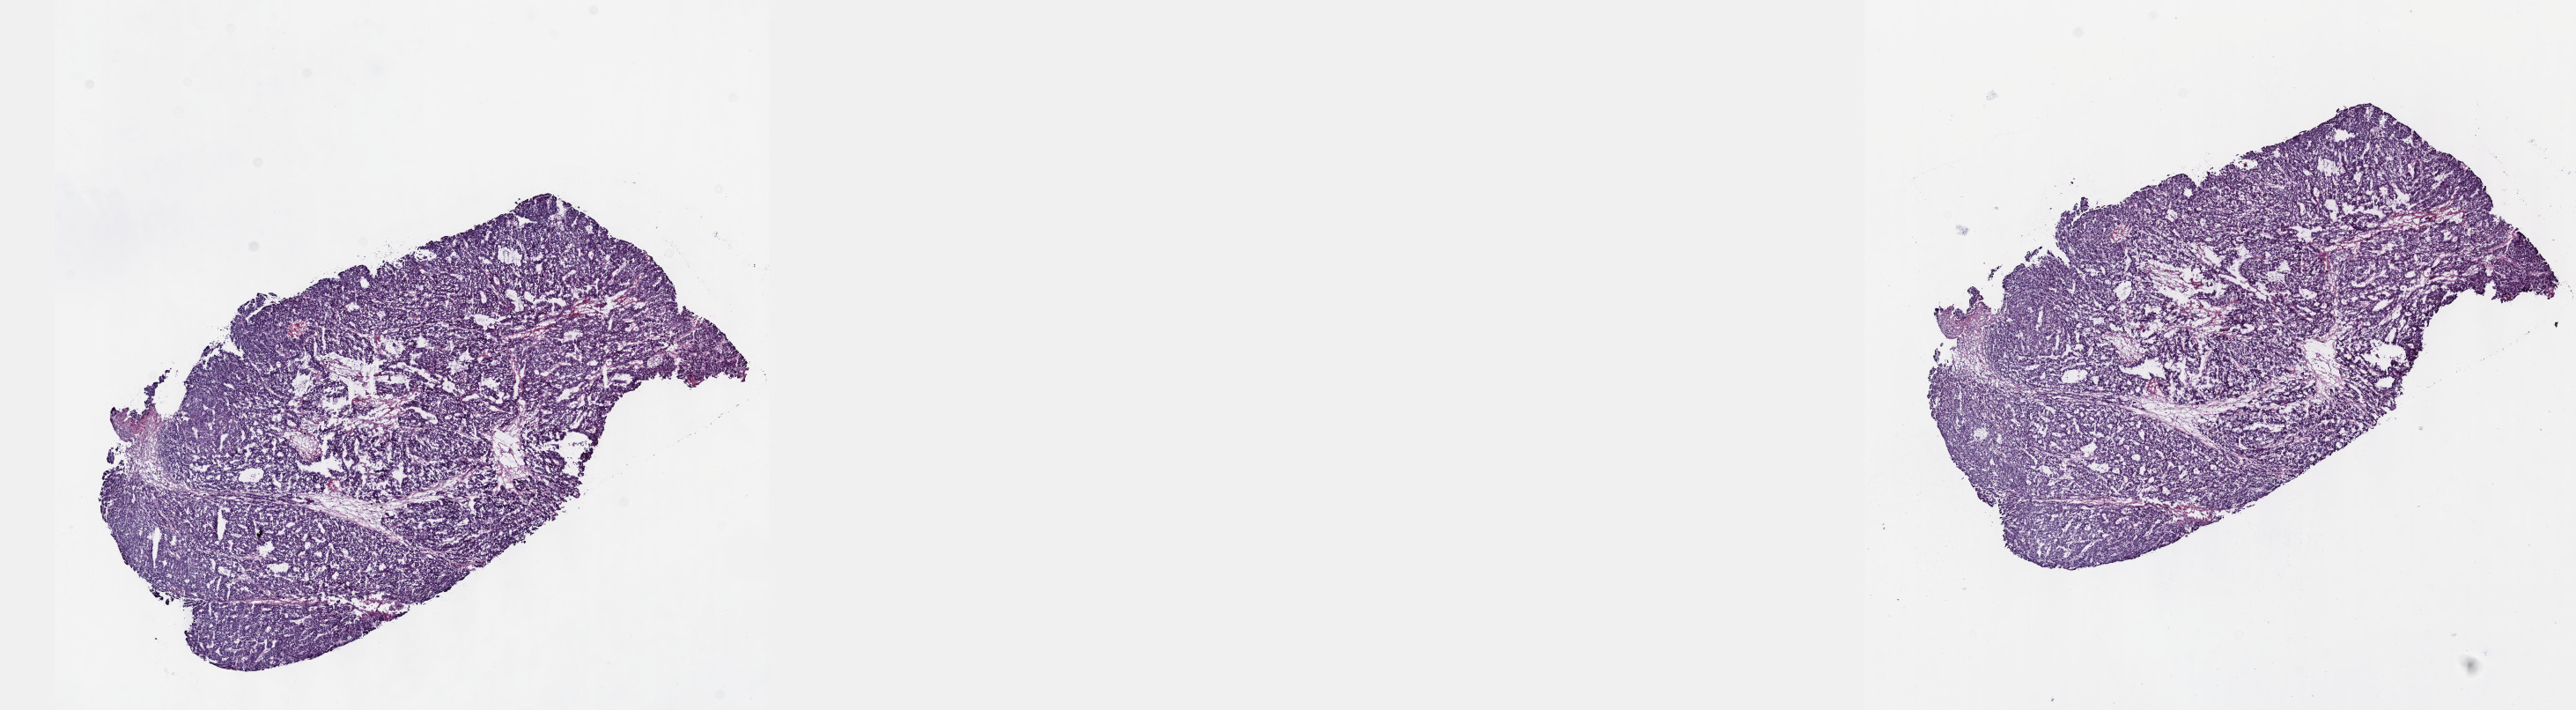
H&E whole-slide image — low-resolution overview of the scanned area, about 23.6 x 6.5 mm, frozen section from the top of the tissue portion, primary tumour sample from the liver. Male, age 59 years at initial diagnosis. Histologic grade: G3 (poorly differentiated). Composition of this section per pathologist review: tumour cells 90%, tumour nuclei 95%, normal cells 0%, stromal cells 10%, necrosis 0%. Infiltration values recorded for this section: lymphocyte infiltration 0%, monocyte infiltration 0%, neutrophil infiltration 0%.
Diagnosis: Hepatocellular carcinoma, NOS. TNM: T2 N0 M0. AJCC pathologic stage: II (7th edition).